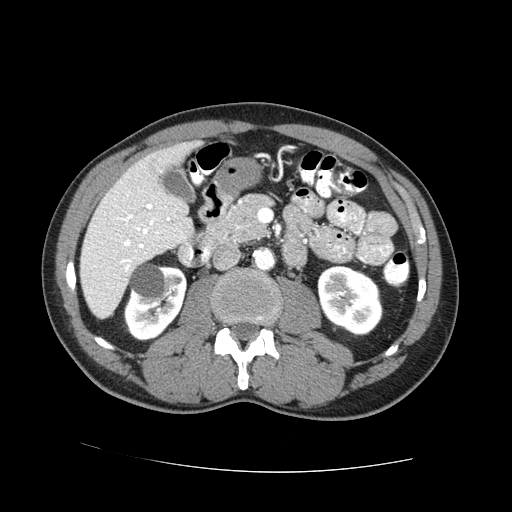
Contrast-enhanced abdominal CT (liver protocol), one axial slice. Slice 24 of 73 in the series (ordered by position). One of 2 acquisitions stored at this slice position. Soft-tissue window (W 400 / L 40 HU). 512 × 512 image matrix, field of view 380 × 380 mm. From the clinical record (not read from this slice): diagnosis: hepatocellular carcinoma (patient treated with transarterial chemoembolisation; whether this scan precedes or follows treatment is not stated here); TNM stage (as recorded): Stage-IVA; Child-Pugh class: A; tumour differentiation: no biopsy; tumour nodularity: uninodular.
Structures marked on this image (semi-automatically segmented with operator editing):
- liver parenchyma outside the tumour (the mass and vessels are separate outlines, so this box may not span the whole liver): bounding box (x1, y1, x2, y2) in pixels: (80, 140, 200, 318)
- liver vessels: (118, 204, 170, 271)